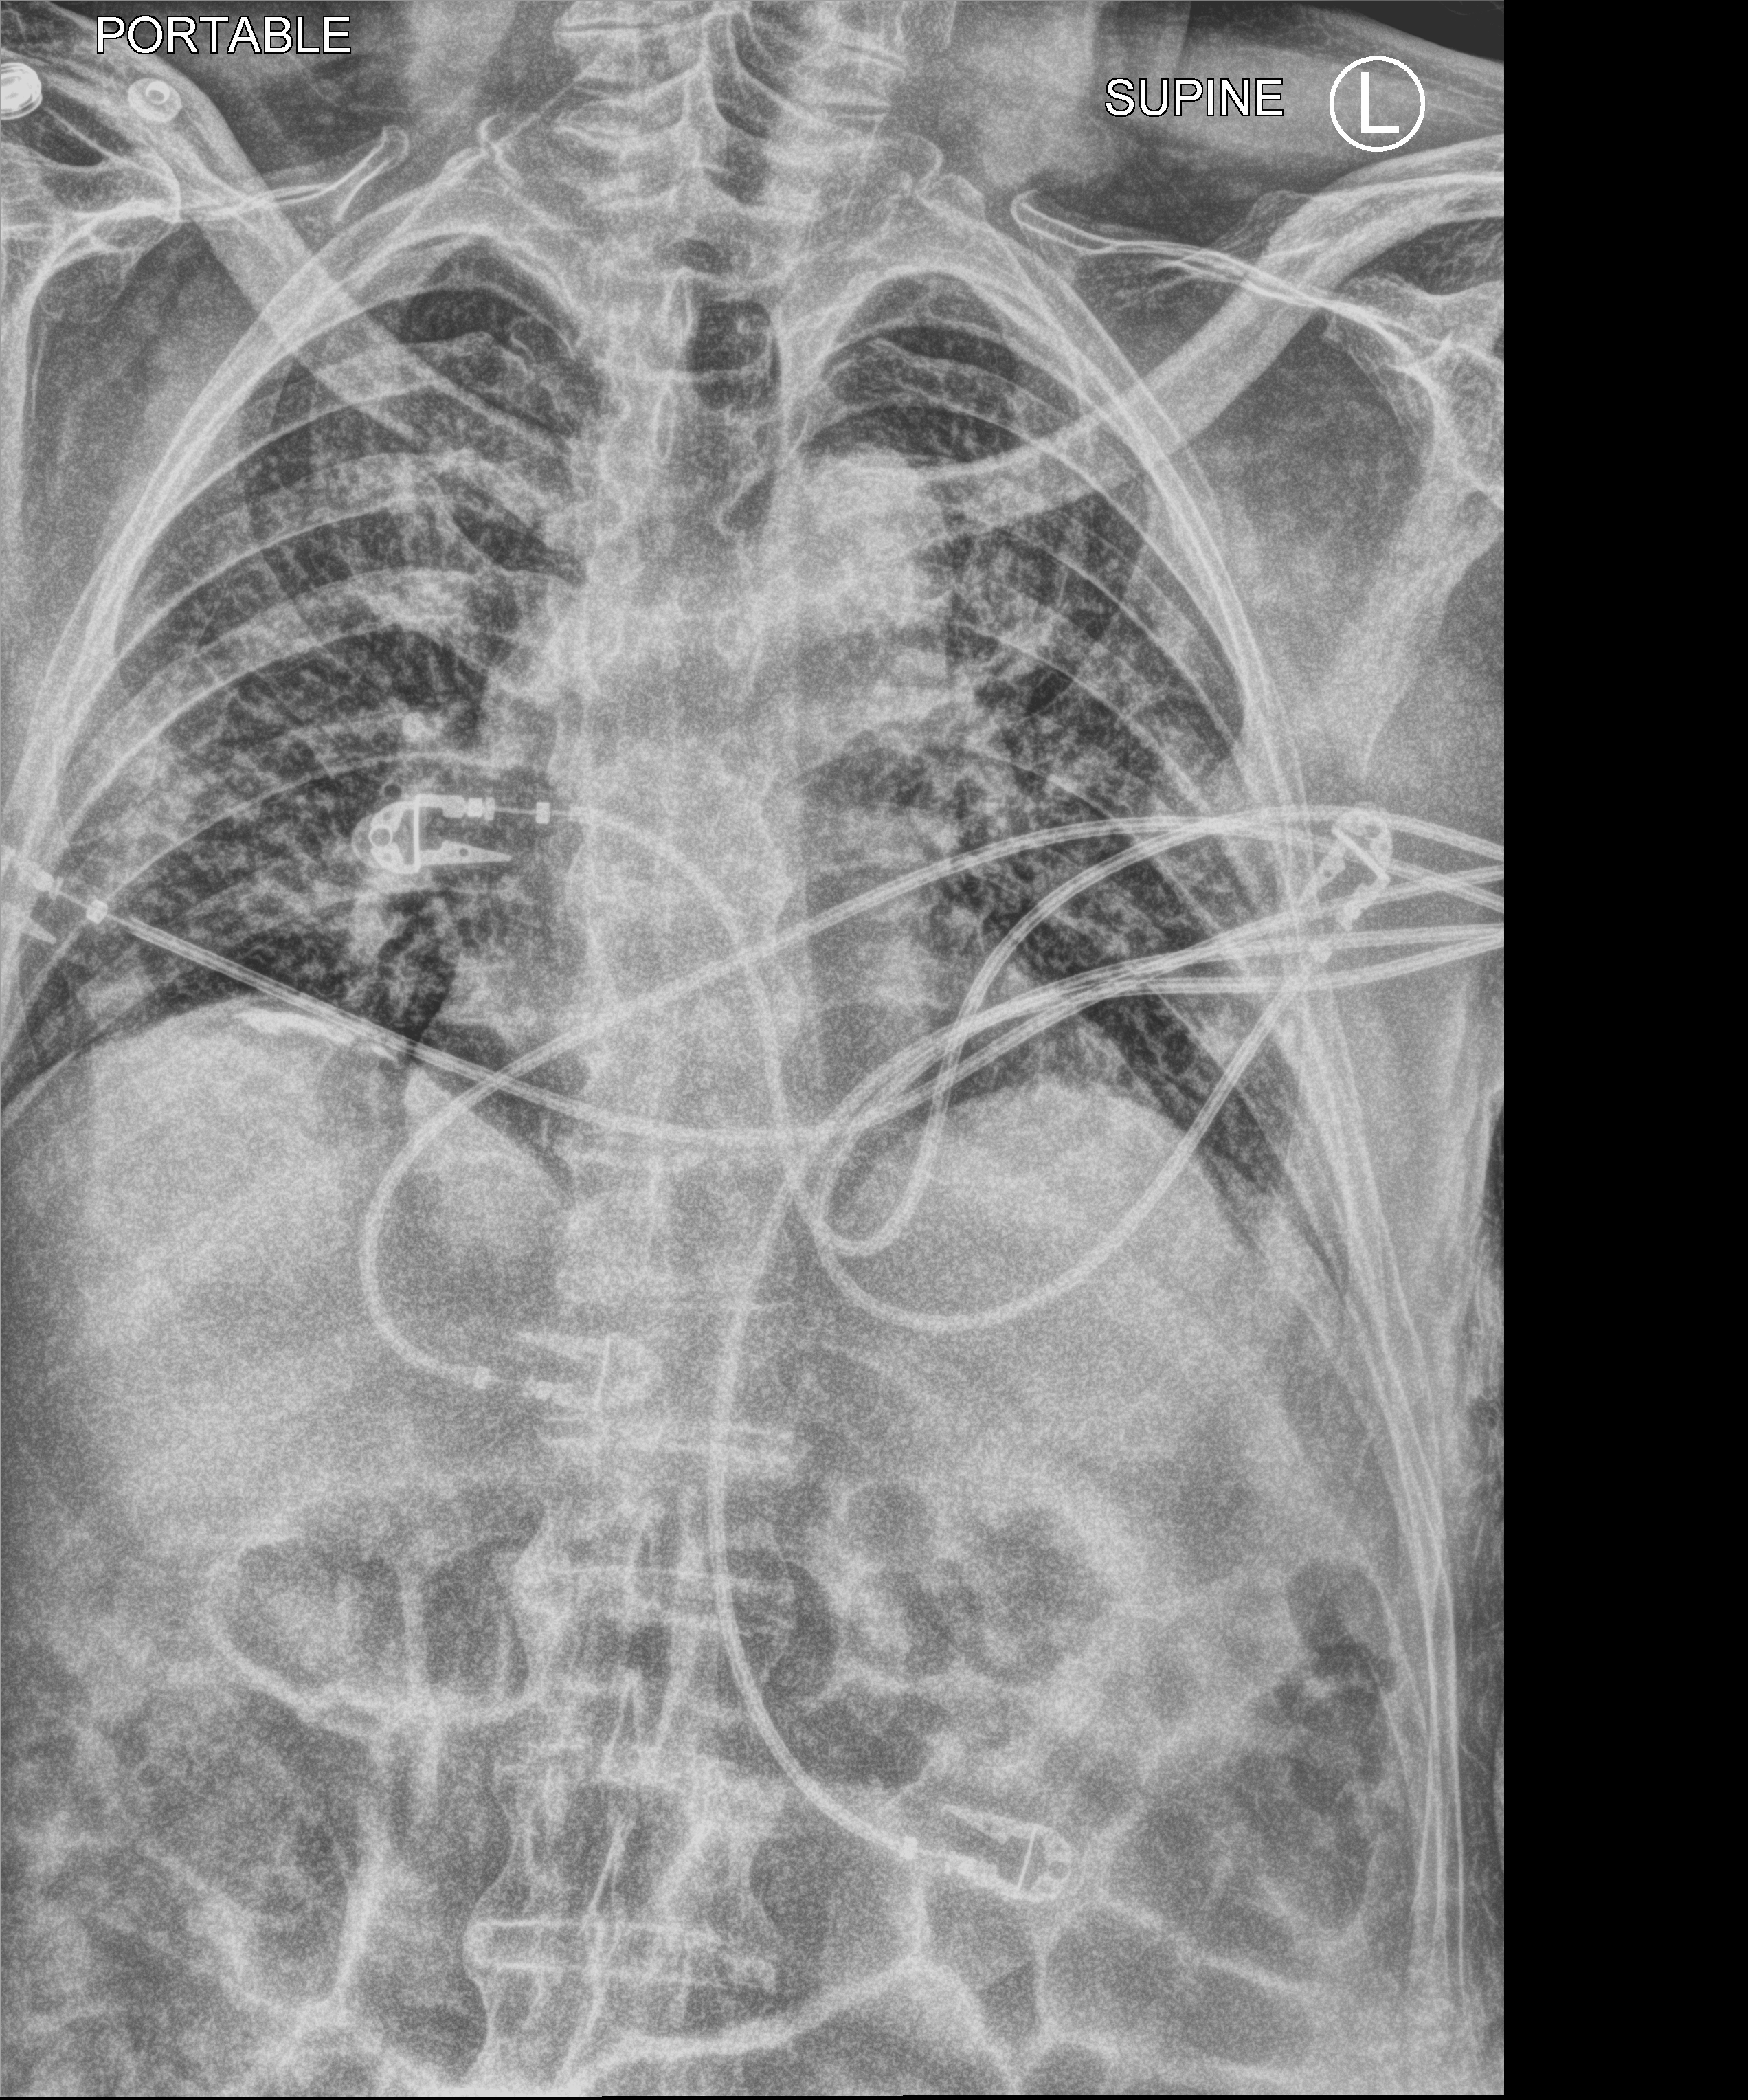
Portable chest radiograph; anteroposterior (AP) projection. Patient hospitalised with COVID-19; male, aged 75–90 years.
Admission-level facts for this patient (not findings on this image; timing relative to this image not recorded): admitted to intensive care during this hospital stay: no; mechanically ventilated during this hospital stay: no.